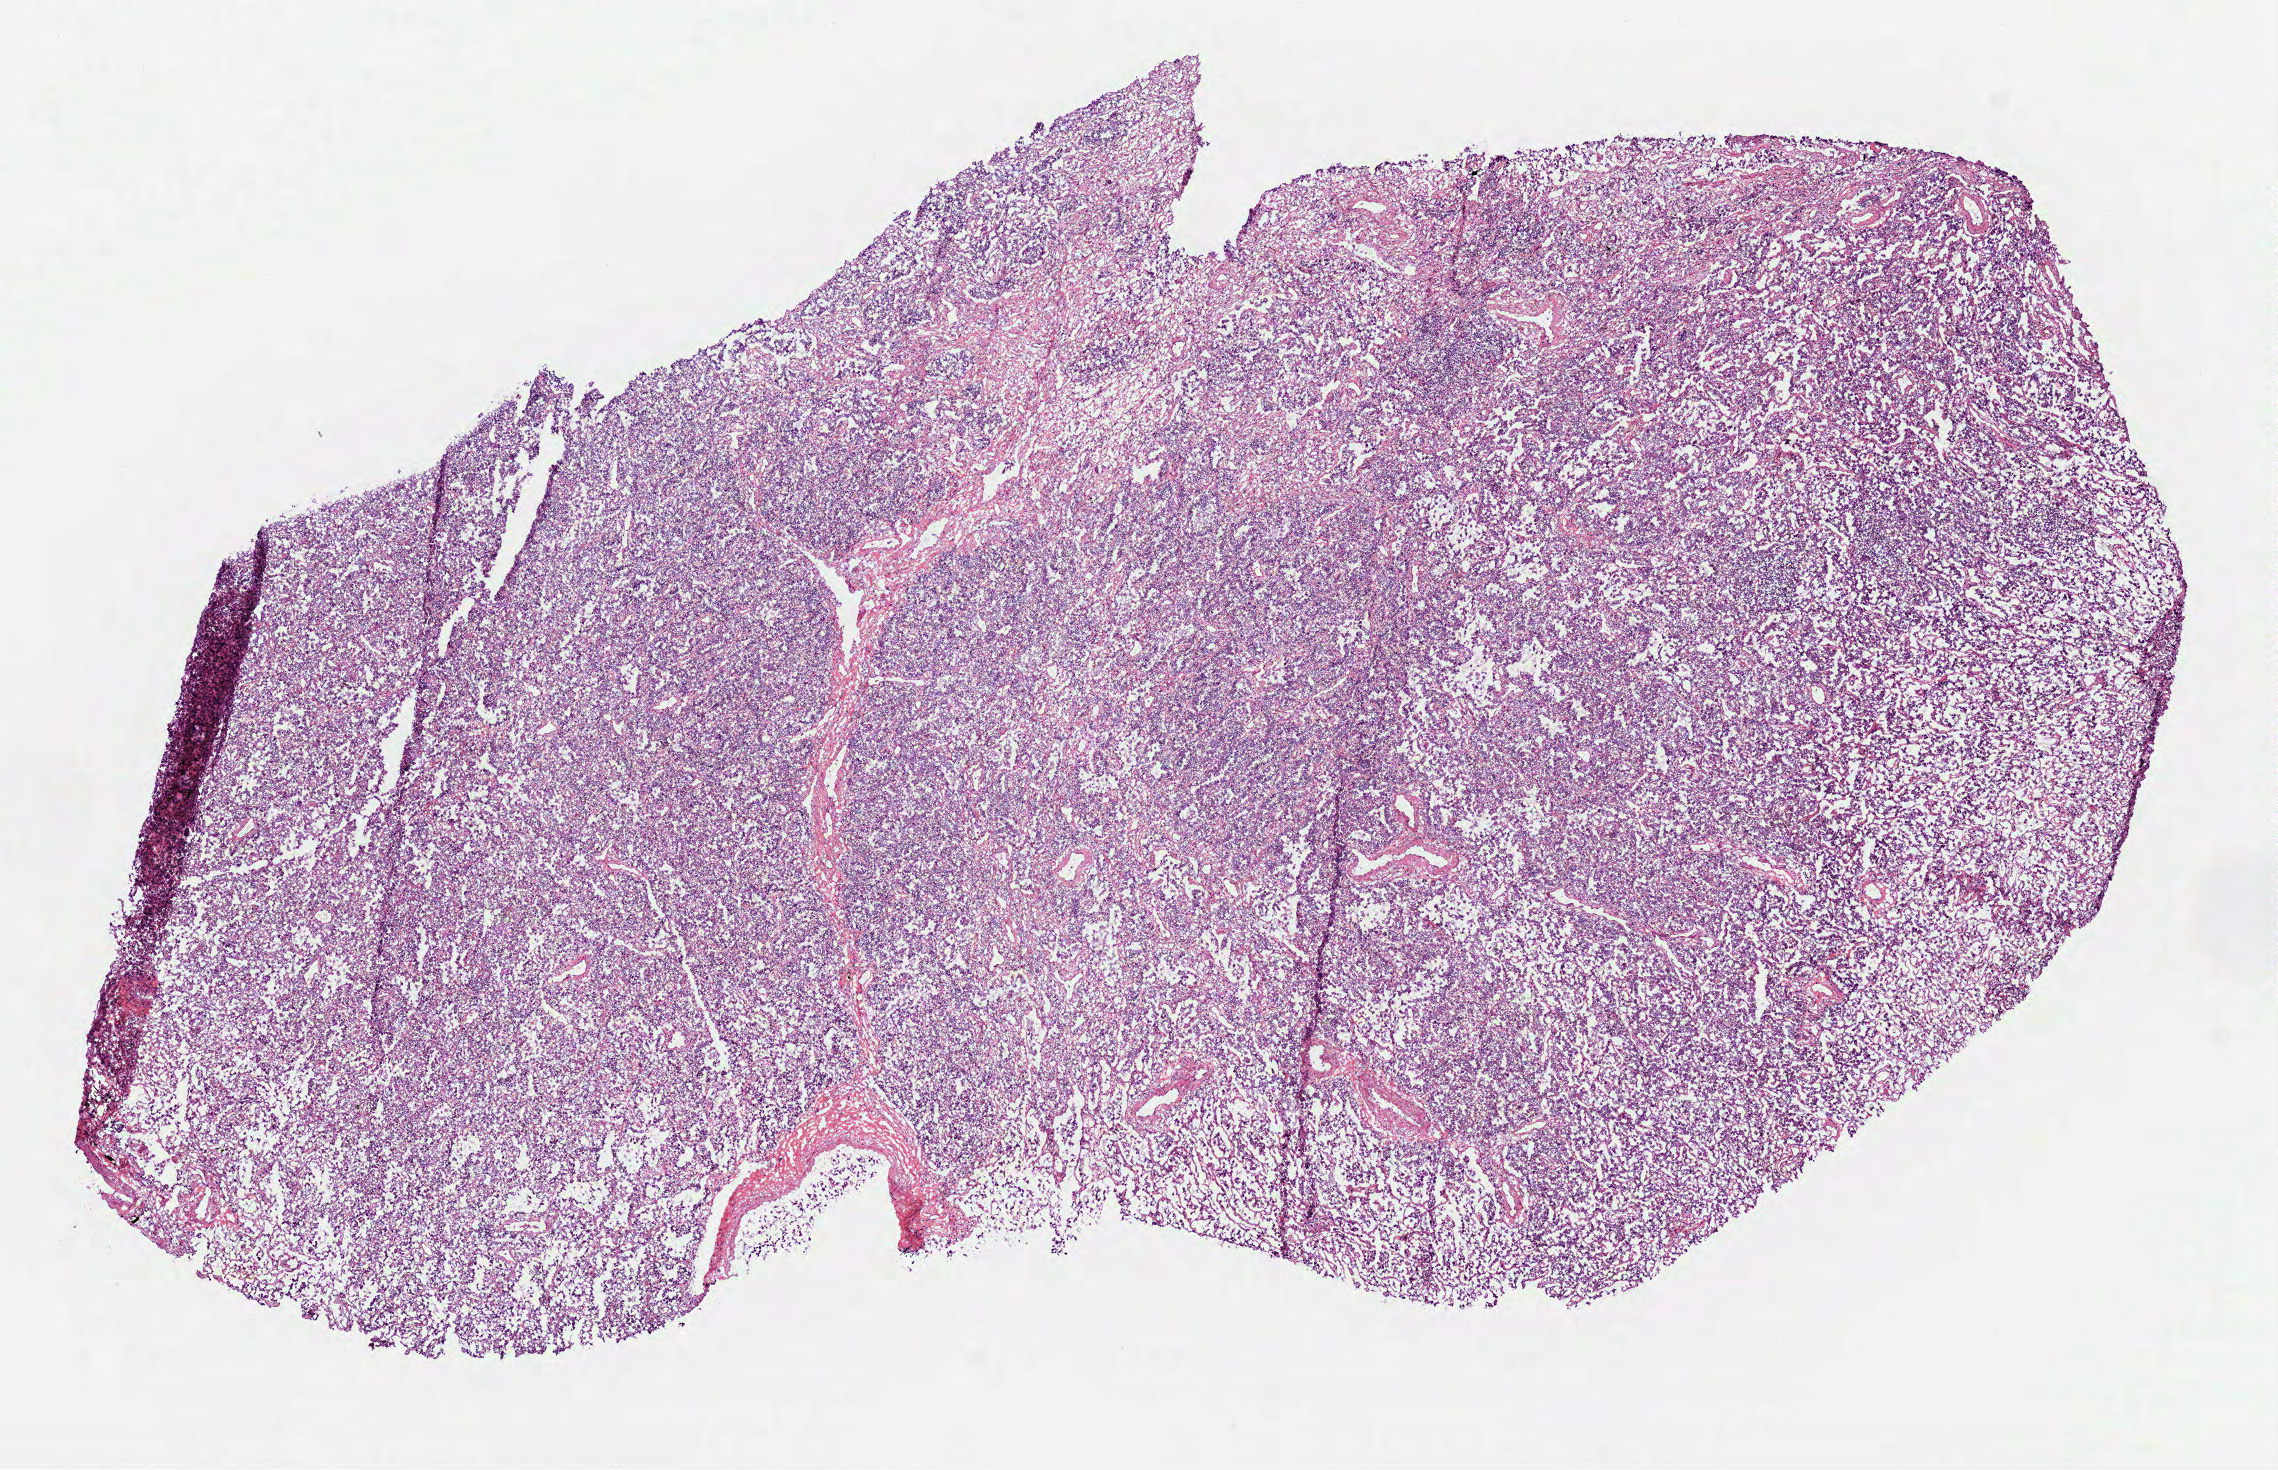
H&E-stained whole-slide image, low-resolution overview of the scanned area, about 9.2 x 5.9 mm; frozen section from the bottom of the tissue portion; primary tumour sample from the lung. Female, age 58 years at initial diagnosis. Slide review estimates, as recorded: tumour cells 90%, tumour nuclei 80%, normal cells 0%, stromal cells 10%, necrosis 0%. Inflammatory infiltration, as recorded: lymphocyte infiltration 5%, monocyte infiltration 2%, neutrophil infiltration 2%.
TNM: T1b N0 M0. Pathologic diagnosis: Bronchiolo-alveolar carcinoma, non-mucinous (lower lobe, lung). AJCC pathologic stage: IA (7th edition).